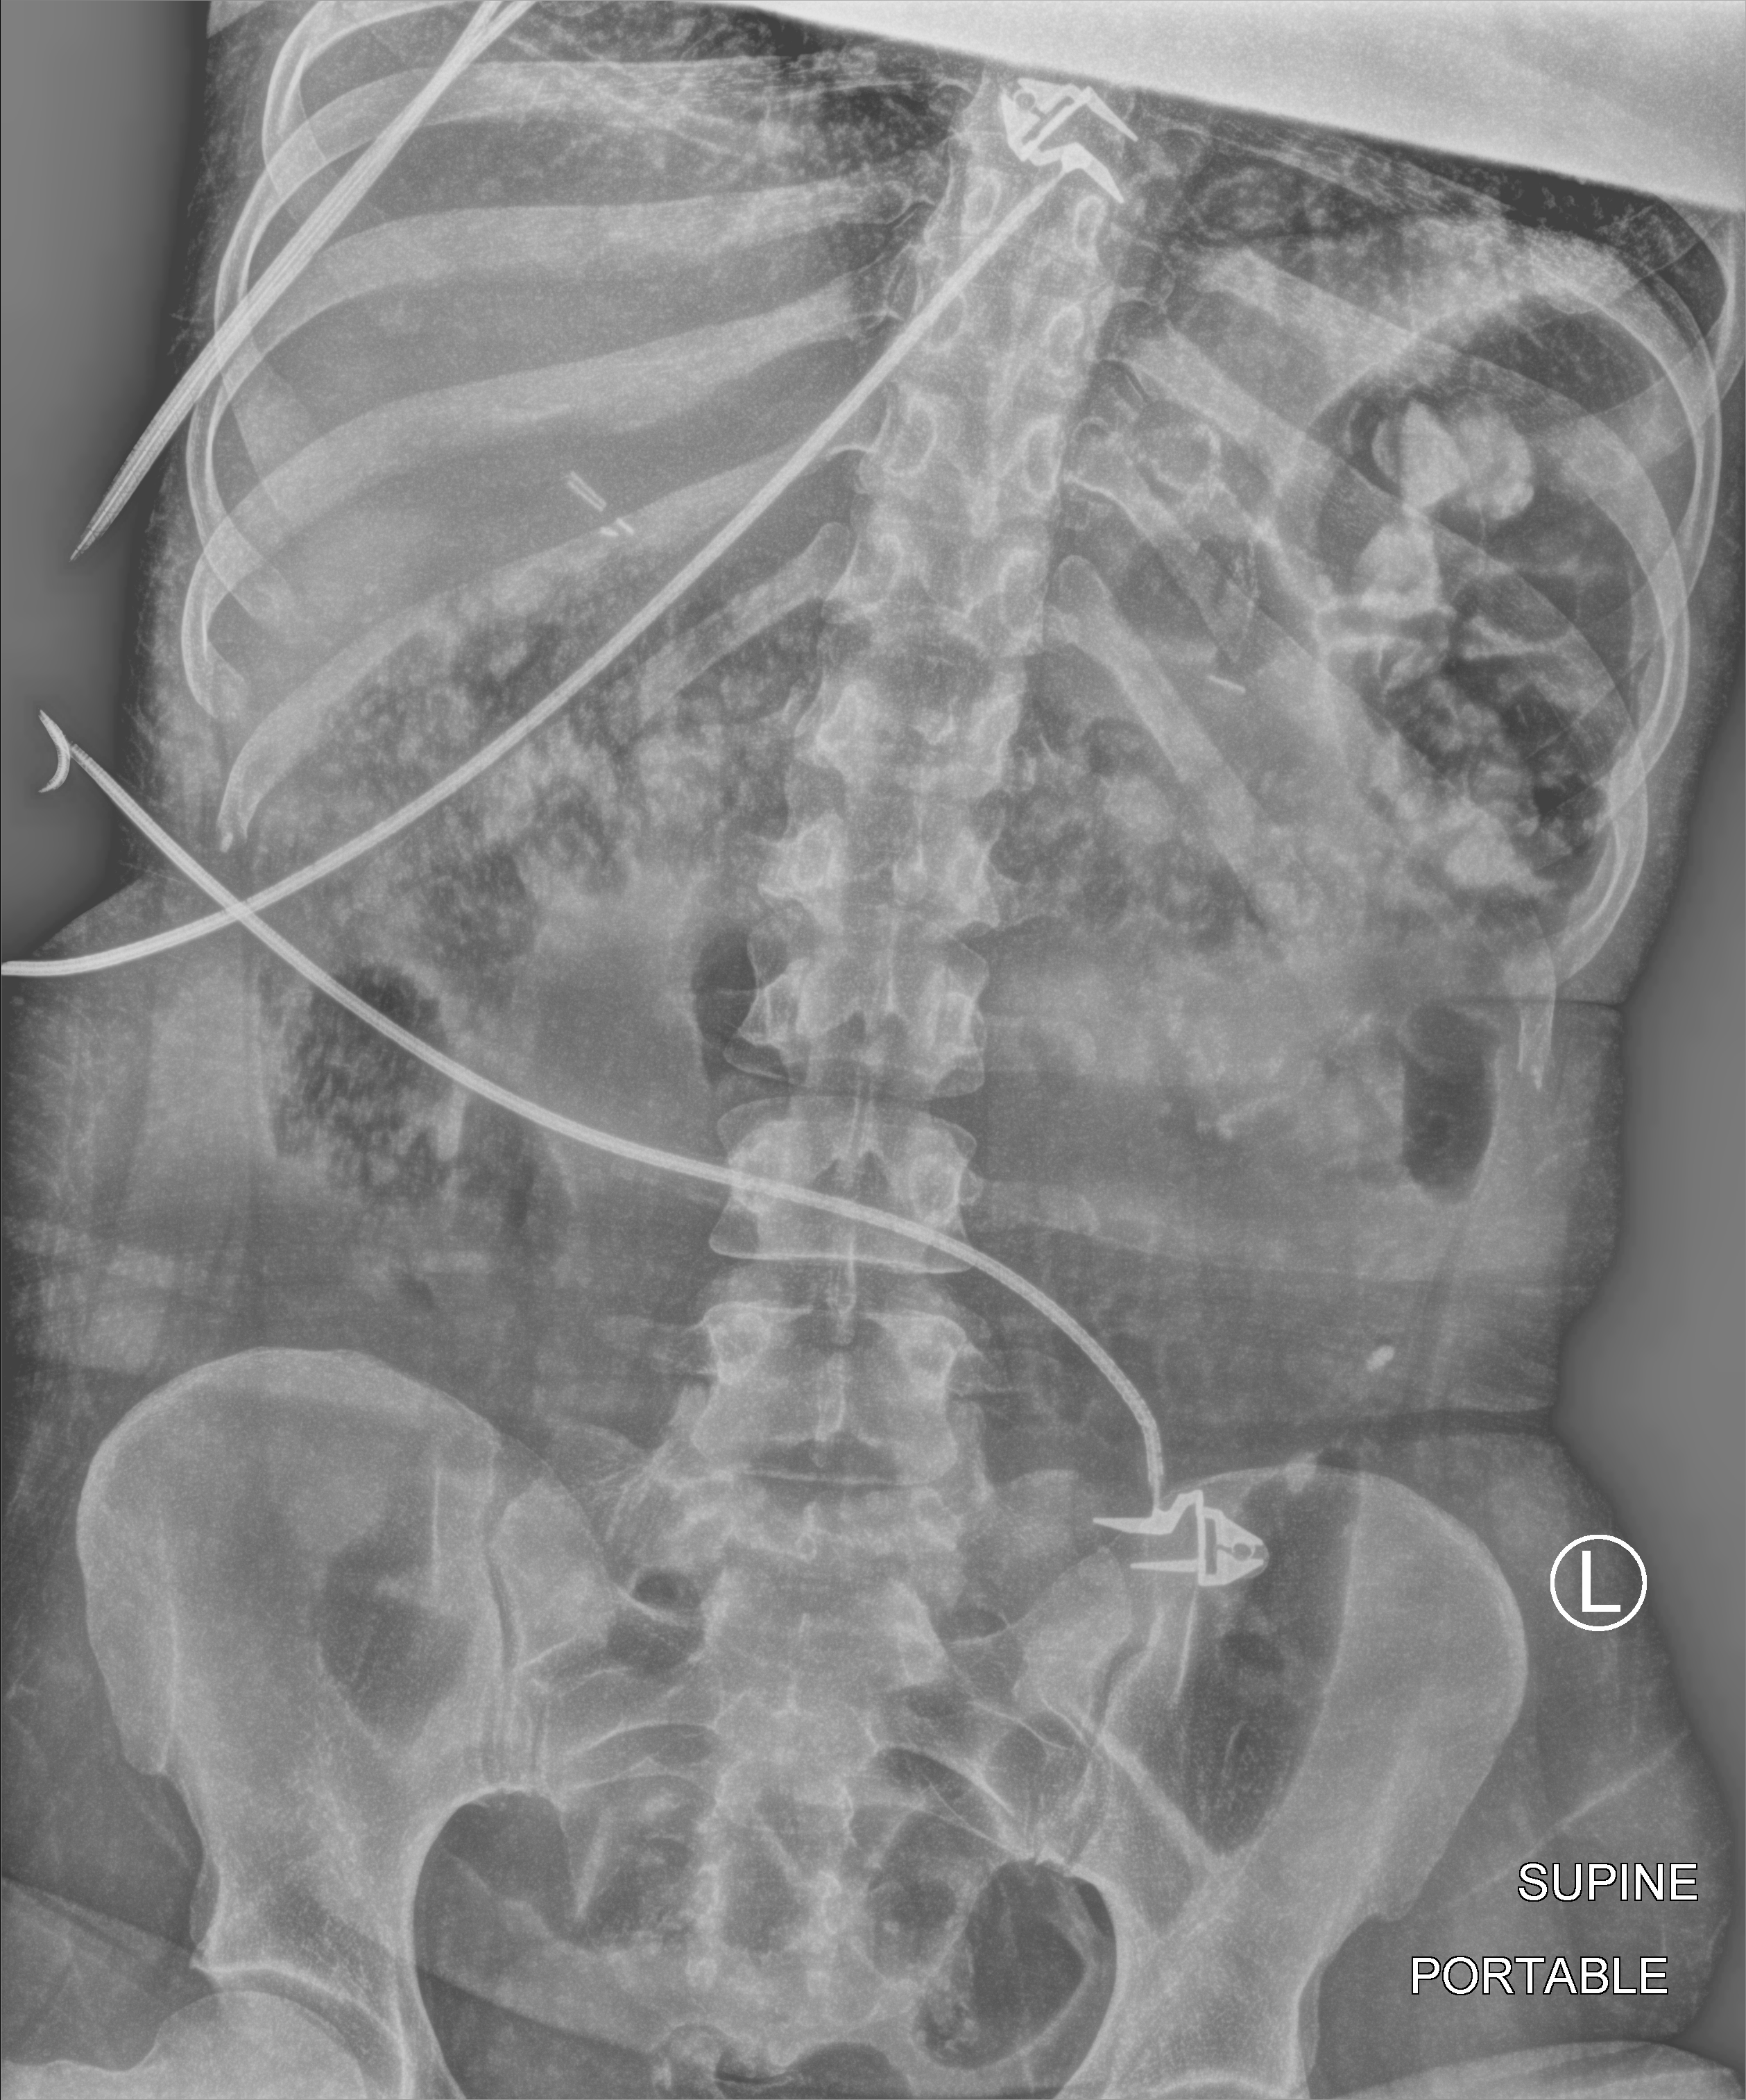
Abdomen X-ray (portable); anteroposterior (AP) projection. Female patient hospitalised with COVID-19, age 18–59 years.
Hospital-stay facts (about this admission, not read from this image; timing relative to this image not recorded):
- mechanically ventilated during this hospital stay: no